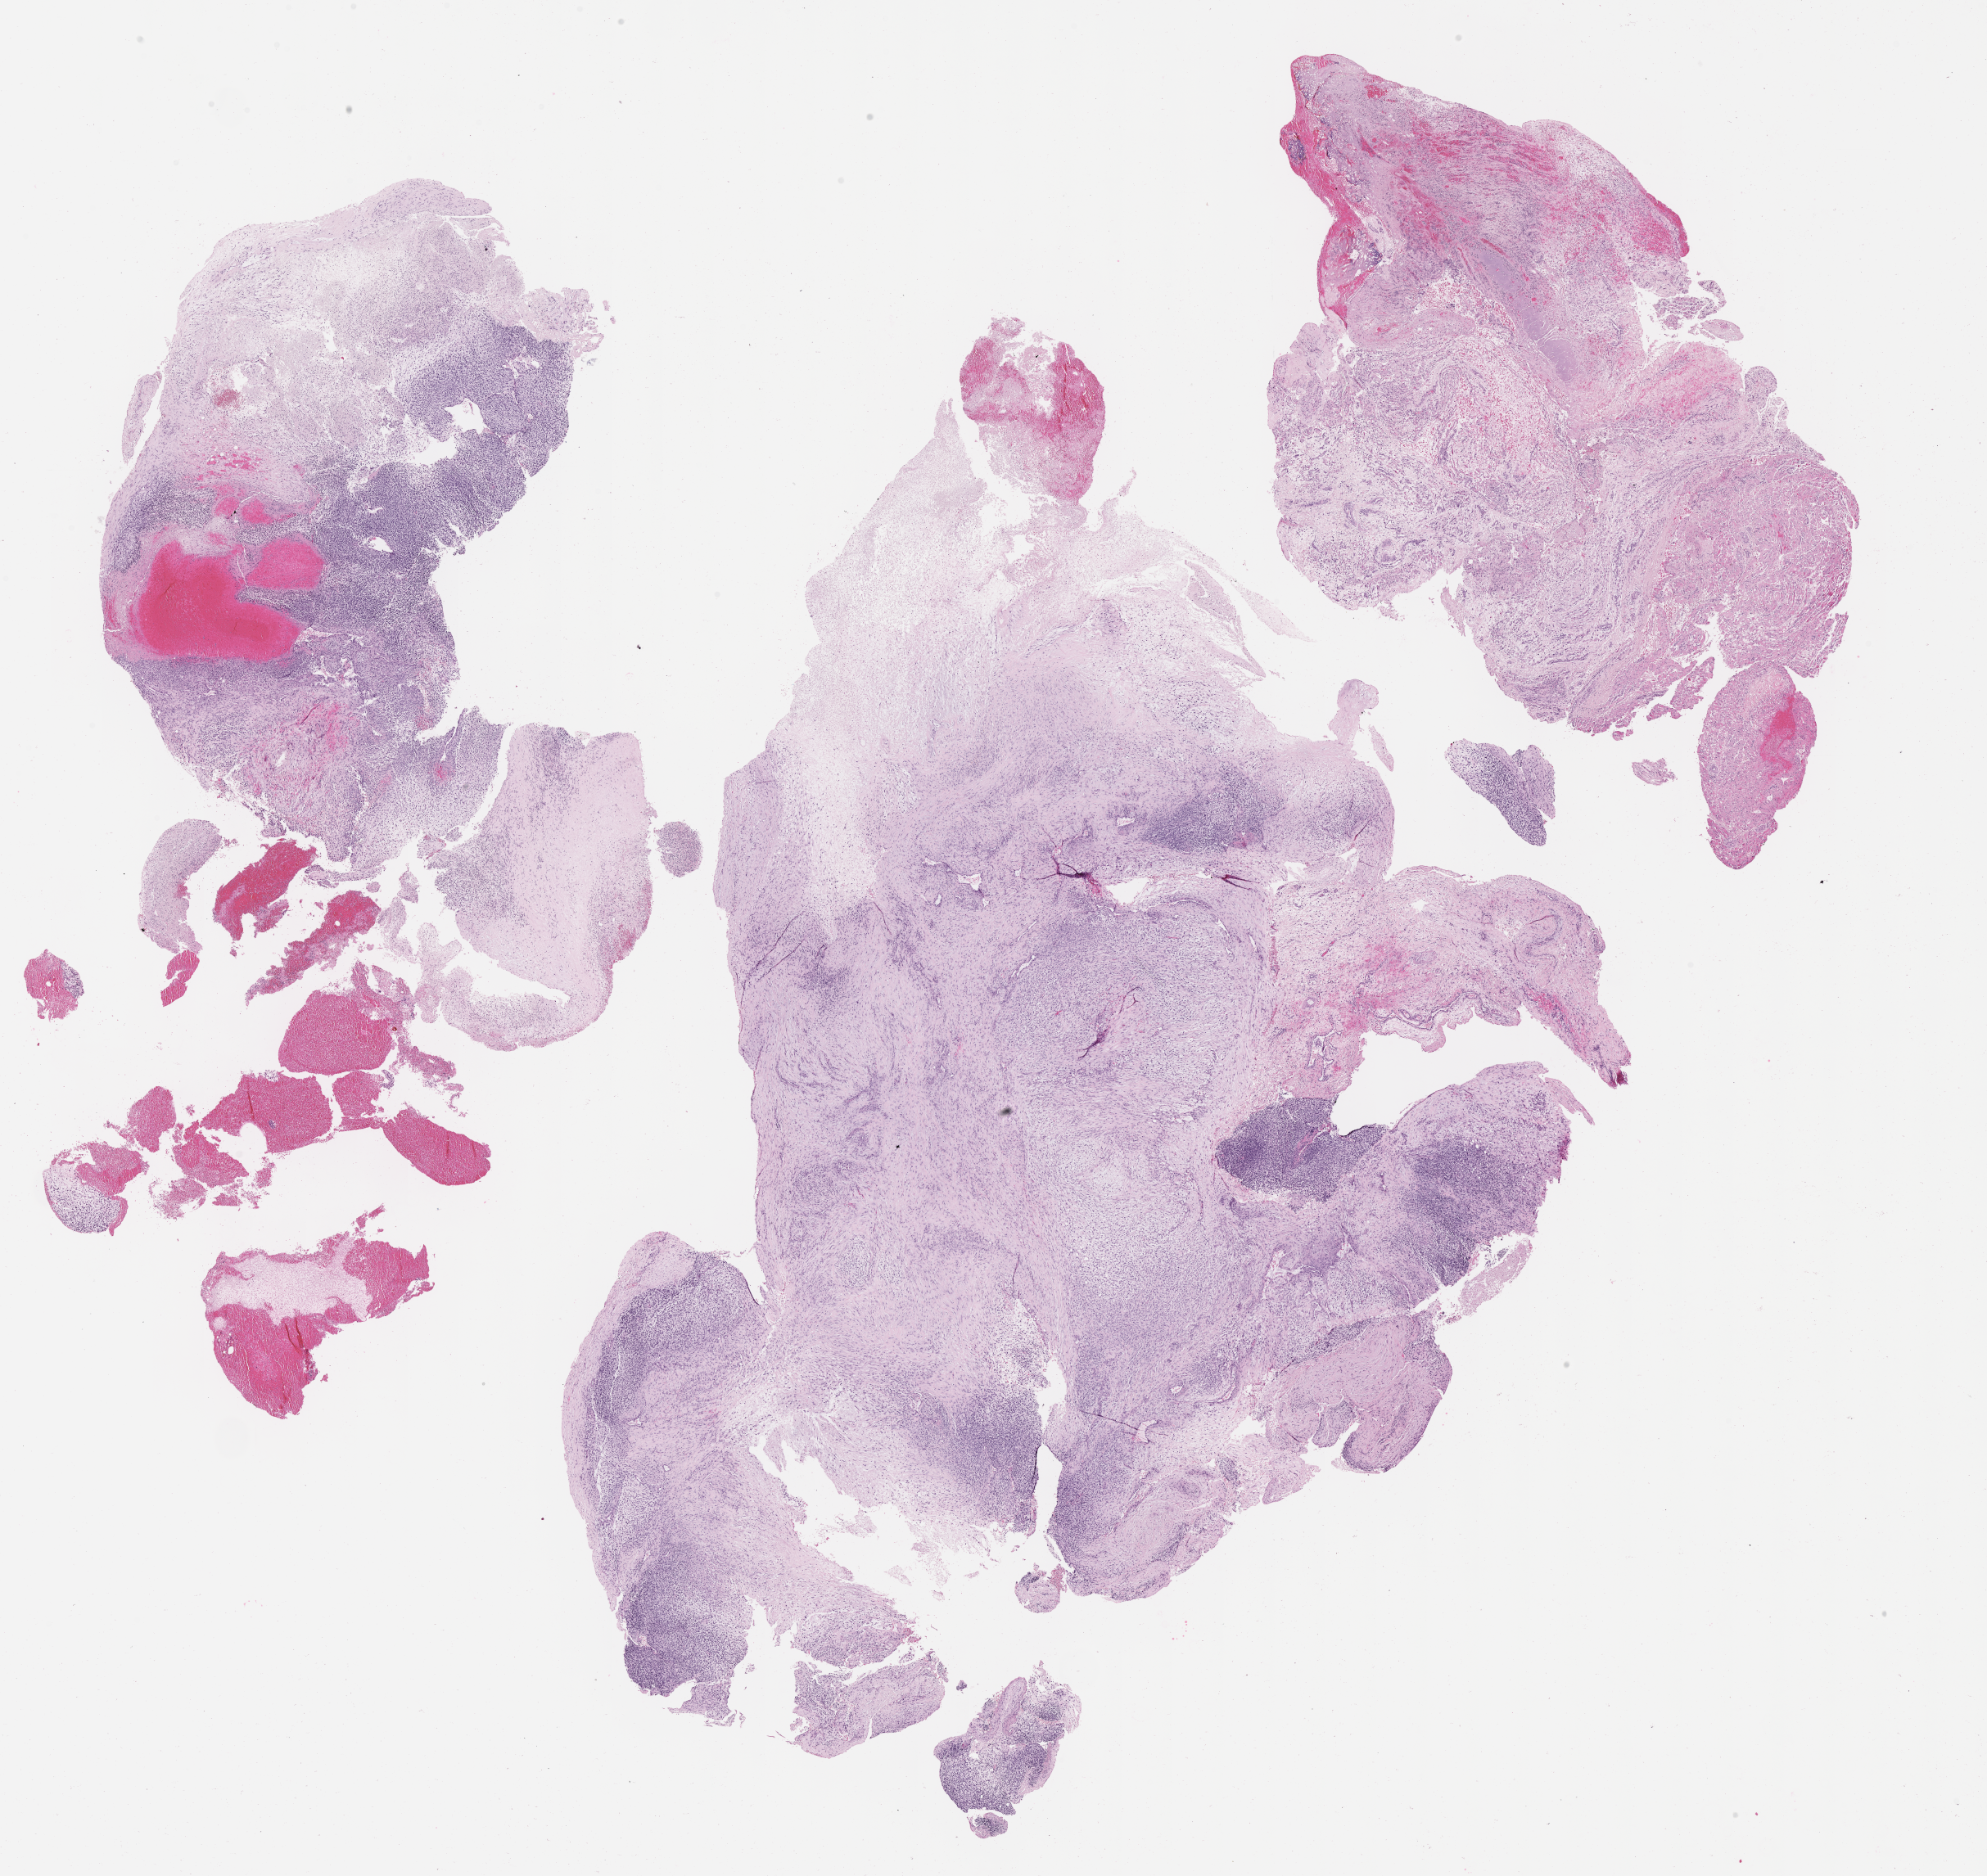
Whole-slide image, haematoxylin and eosin stain of tumor tissue — a low-resolution overview of the entire scanned area, about 19.6 x 18.5 mm, FFPE section, site: soft tissue - neck, right. Patient: male, age 4.9 years at diagnosis.
* metastatic status at presentation (as recorded): metastatic
* diagnosis: rhabdomyosarcoma; histological classification: embryonal rhabdomyosarcoma
* stage (as recorded): 4